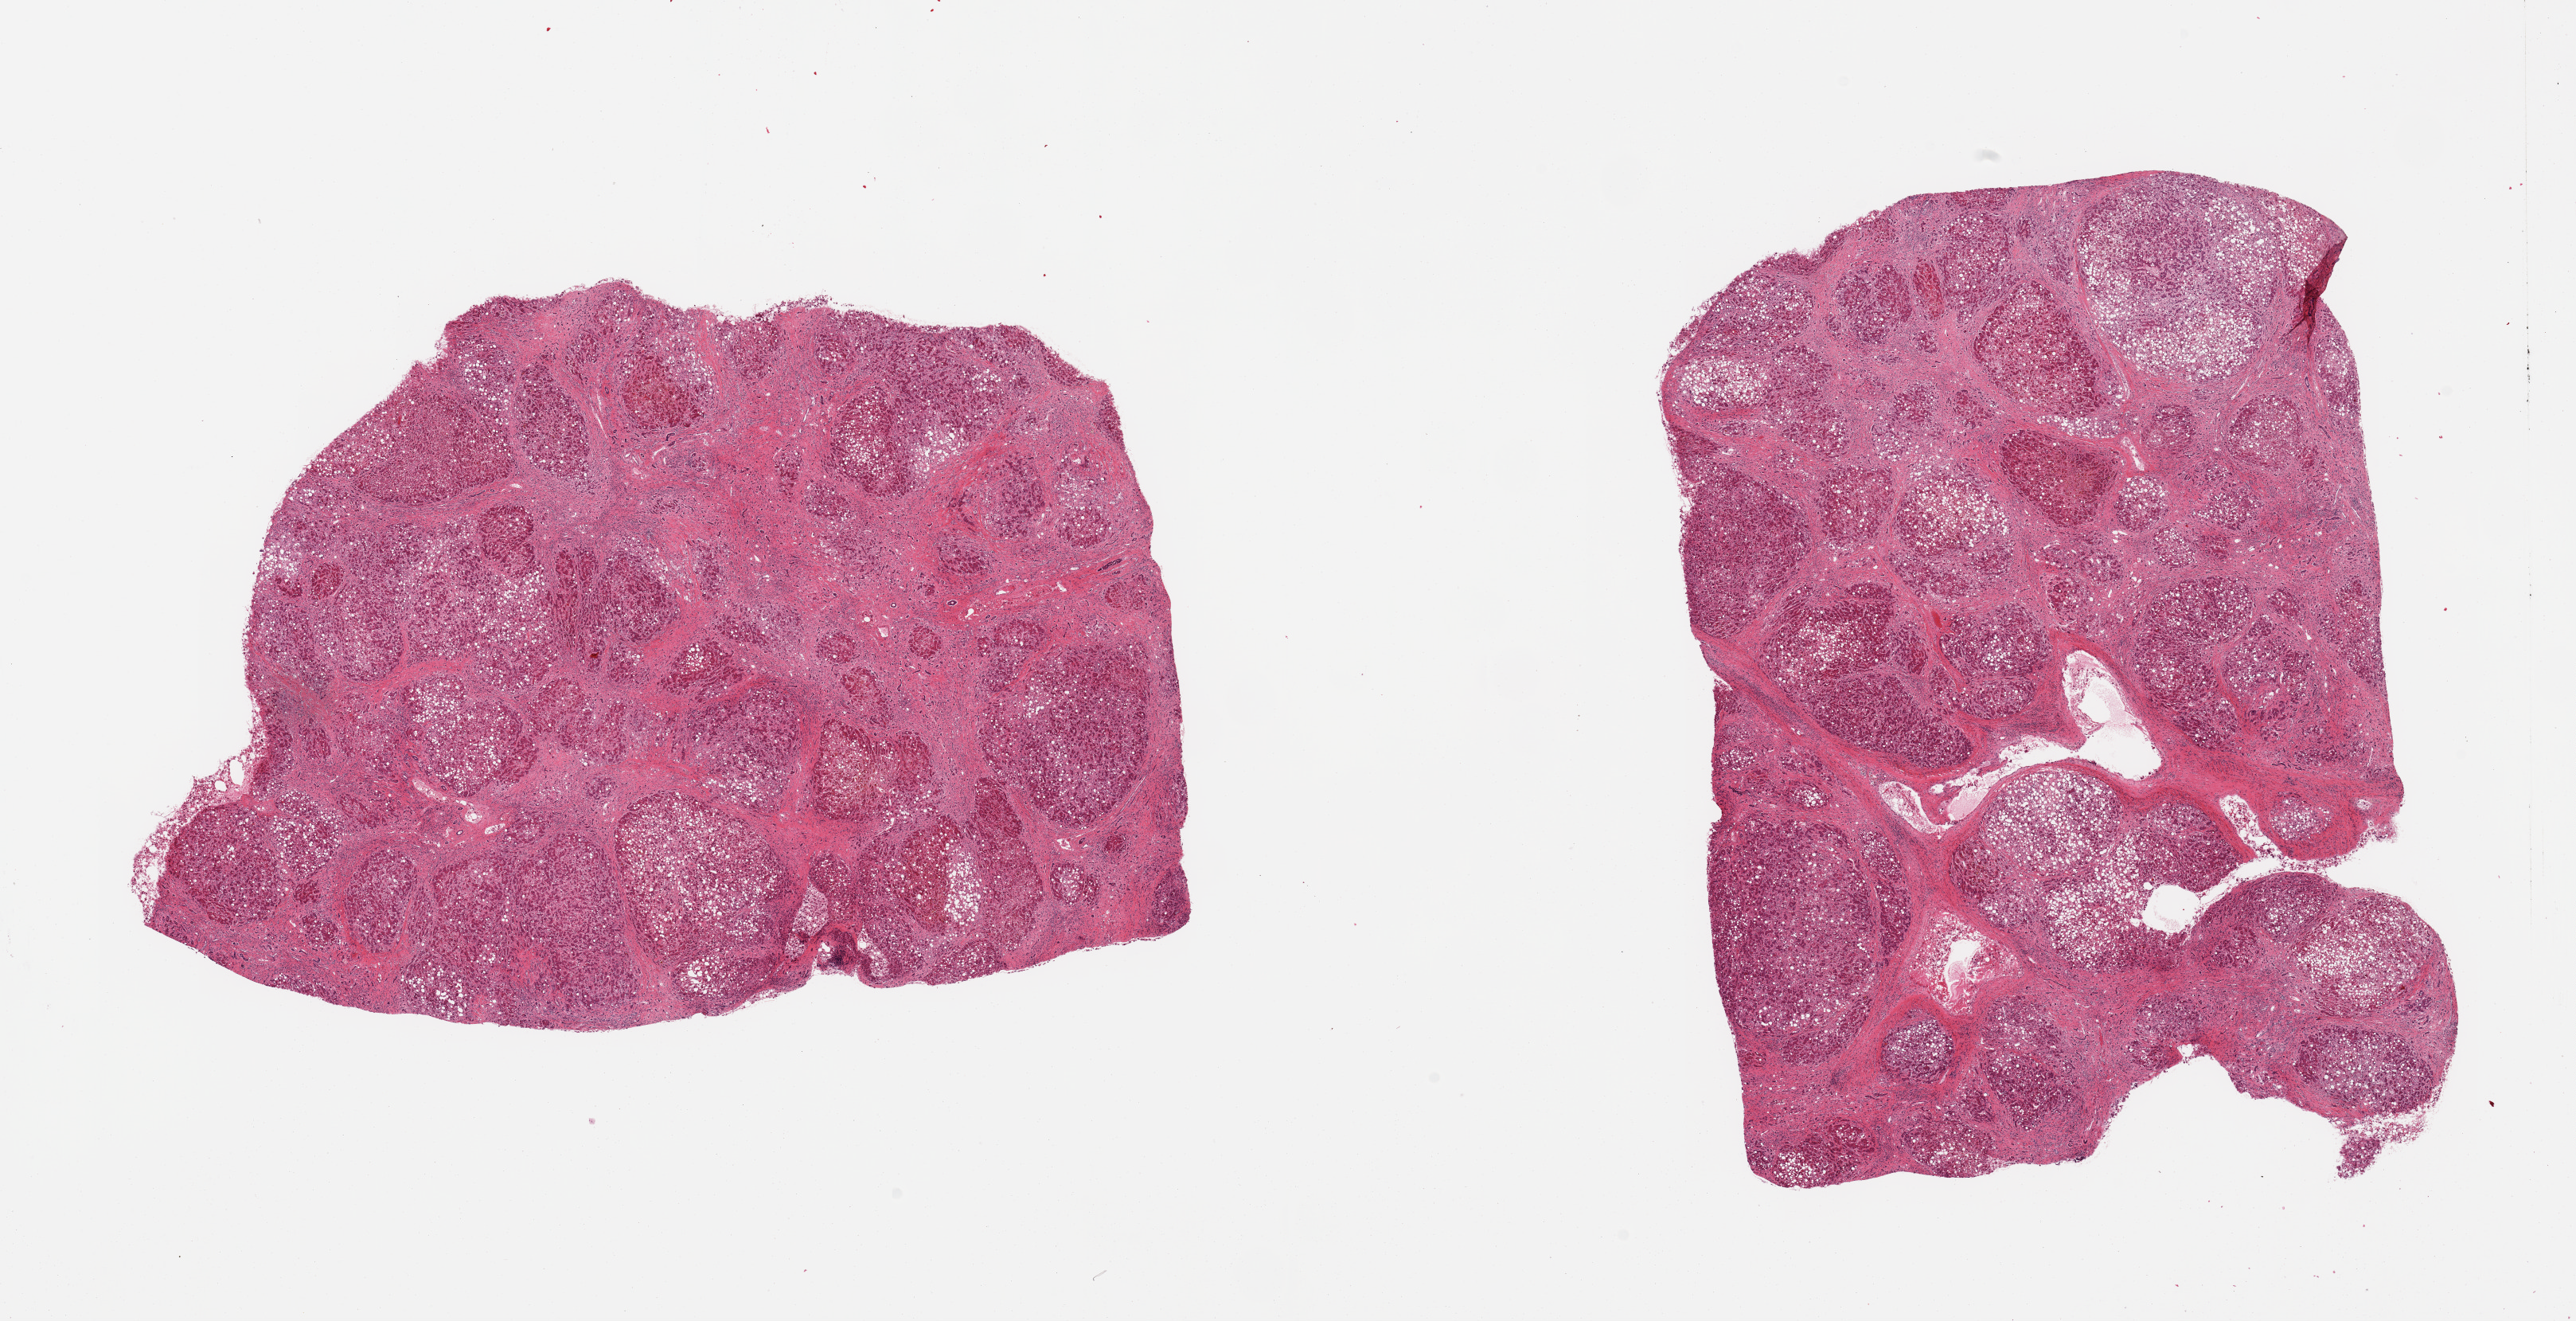
Digitized haematoxylin and eosin-stained section, brightfield — whole scanned area (about 25.6 x 13.1 mm, slide scanned at 20x) shown as a low-resolution overview, PAXgene-fixed, paraffin-embedded tissue, target tissue: liver, donor tissue sample. Donor sex: female.
• reviewer comment on this tissue sample: 2 pieces; cirrhosis, steatosis, Mallory hyaline c/w alcoholic cirrhosis